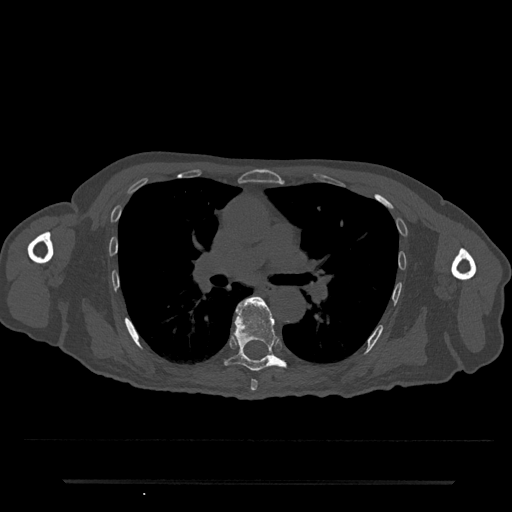
CT including the spine, one axial slice; reconstruction kernel Br40s/3; 120 kVp; bone window (W 1800 / L 400 HU); 0.5 mm slice thickness; 512 × 512 image matrix, field of view 427 × 427 mm. Patient: male, 74 years. From the clinical record (not read from this slice): primary cancer: prostate.
Outlined on this slice (semi-automatically segmented with operator editing):
- T6 vertebra: bounding box <250,379,258,391> (left, top, right, bottom; pixels)
- T7 vertebra: <224,297,286,371>